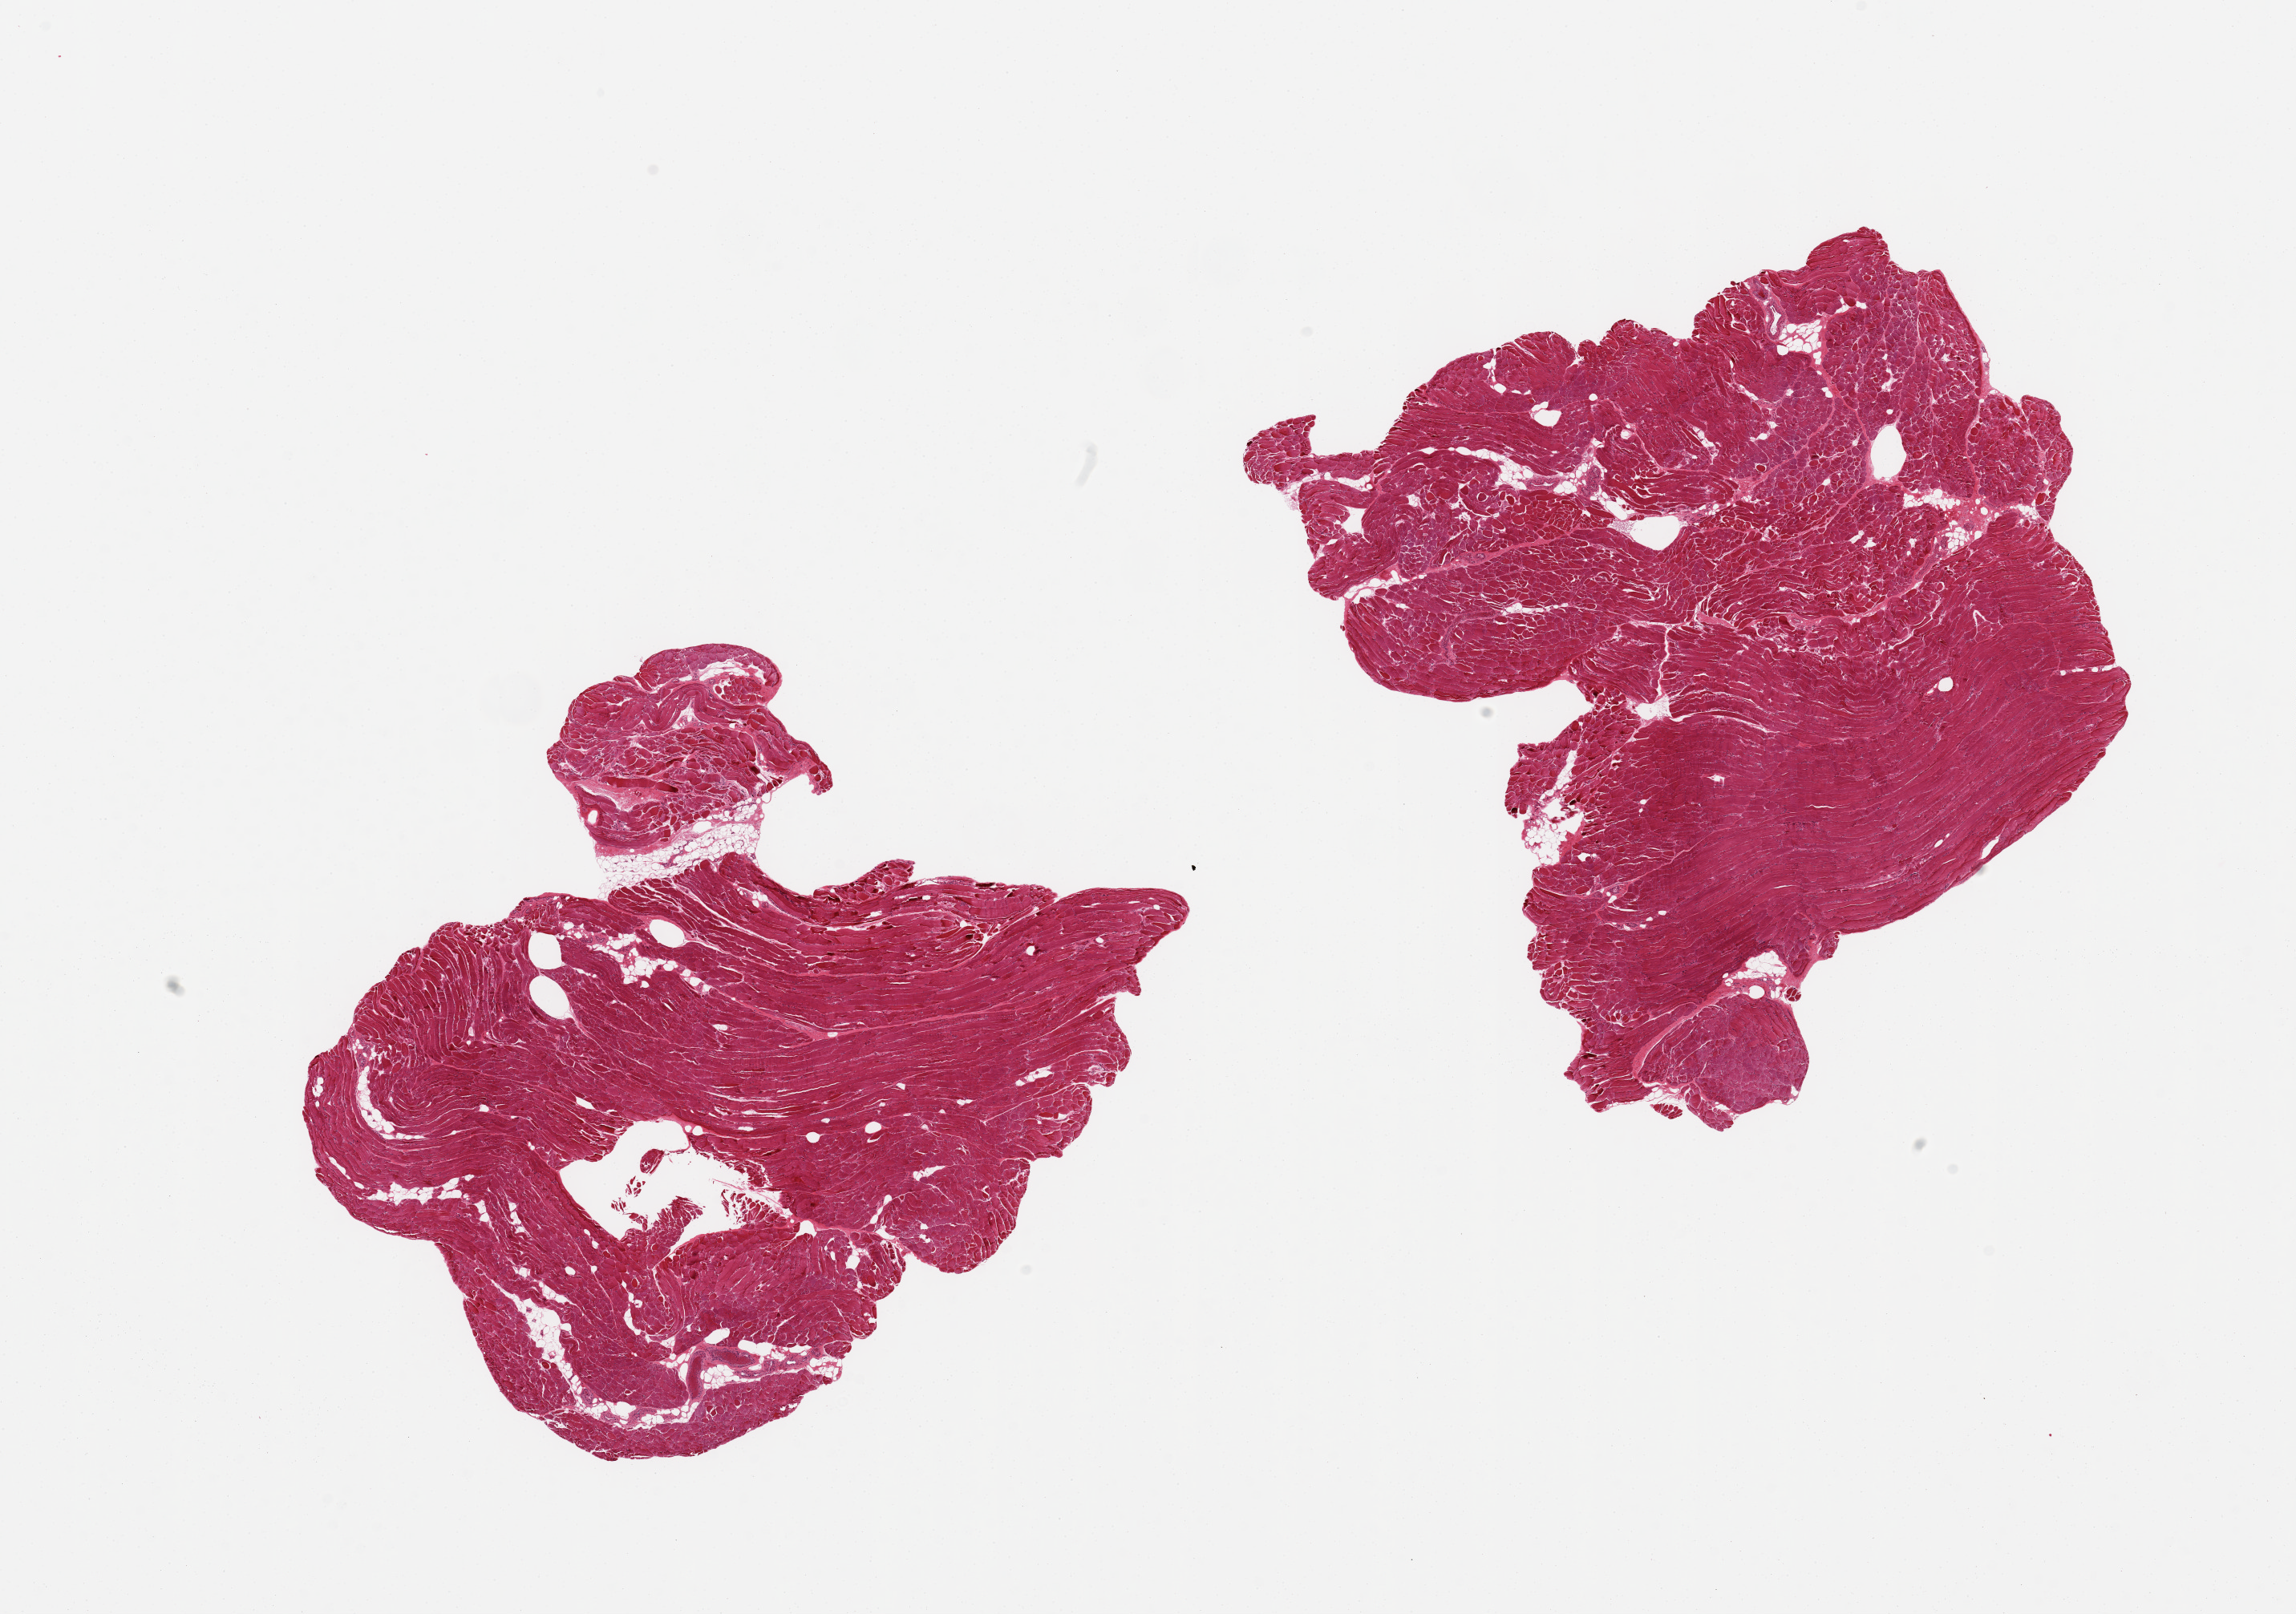
H&E whole-slide image, a low-resolution overview of the entire scanned area, about 22.6 x 15.9 mm; PAXgene-fixed, paraffin-embedded tissue; section of skeletal muscle (target tissue); donor tissue sample. Donor: male.
* pathologist's review note for this sample: 2 pieces, <5% interstitial fat